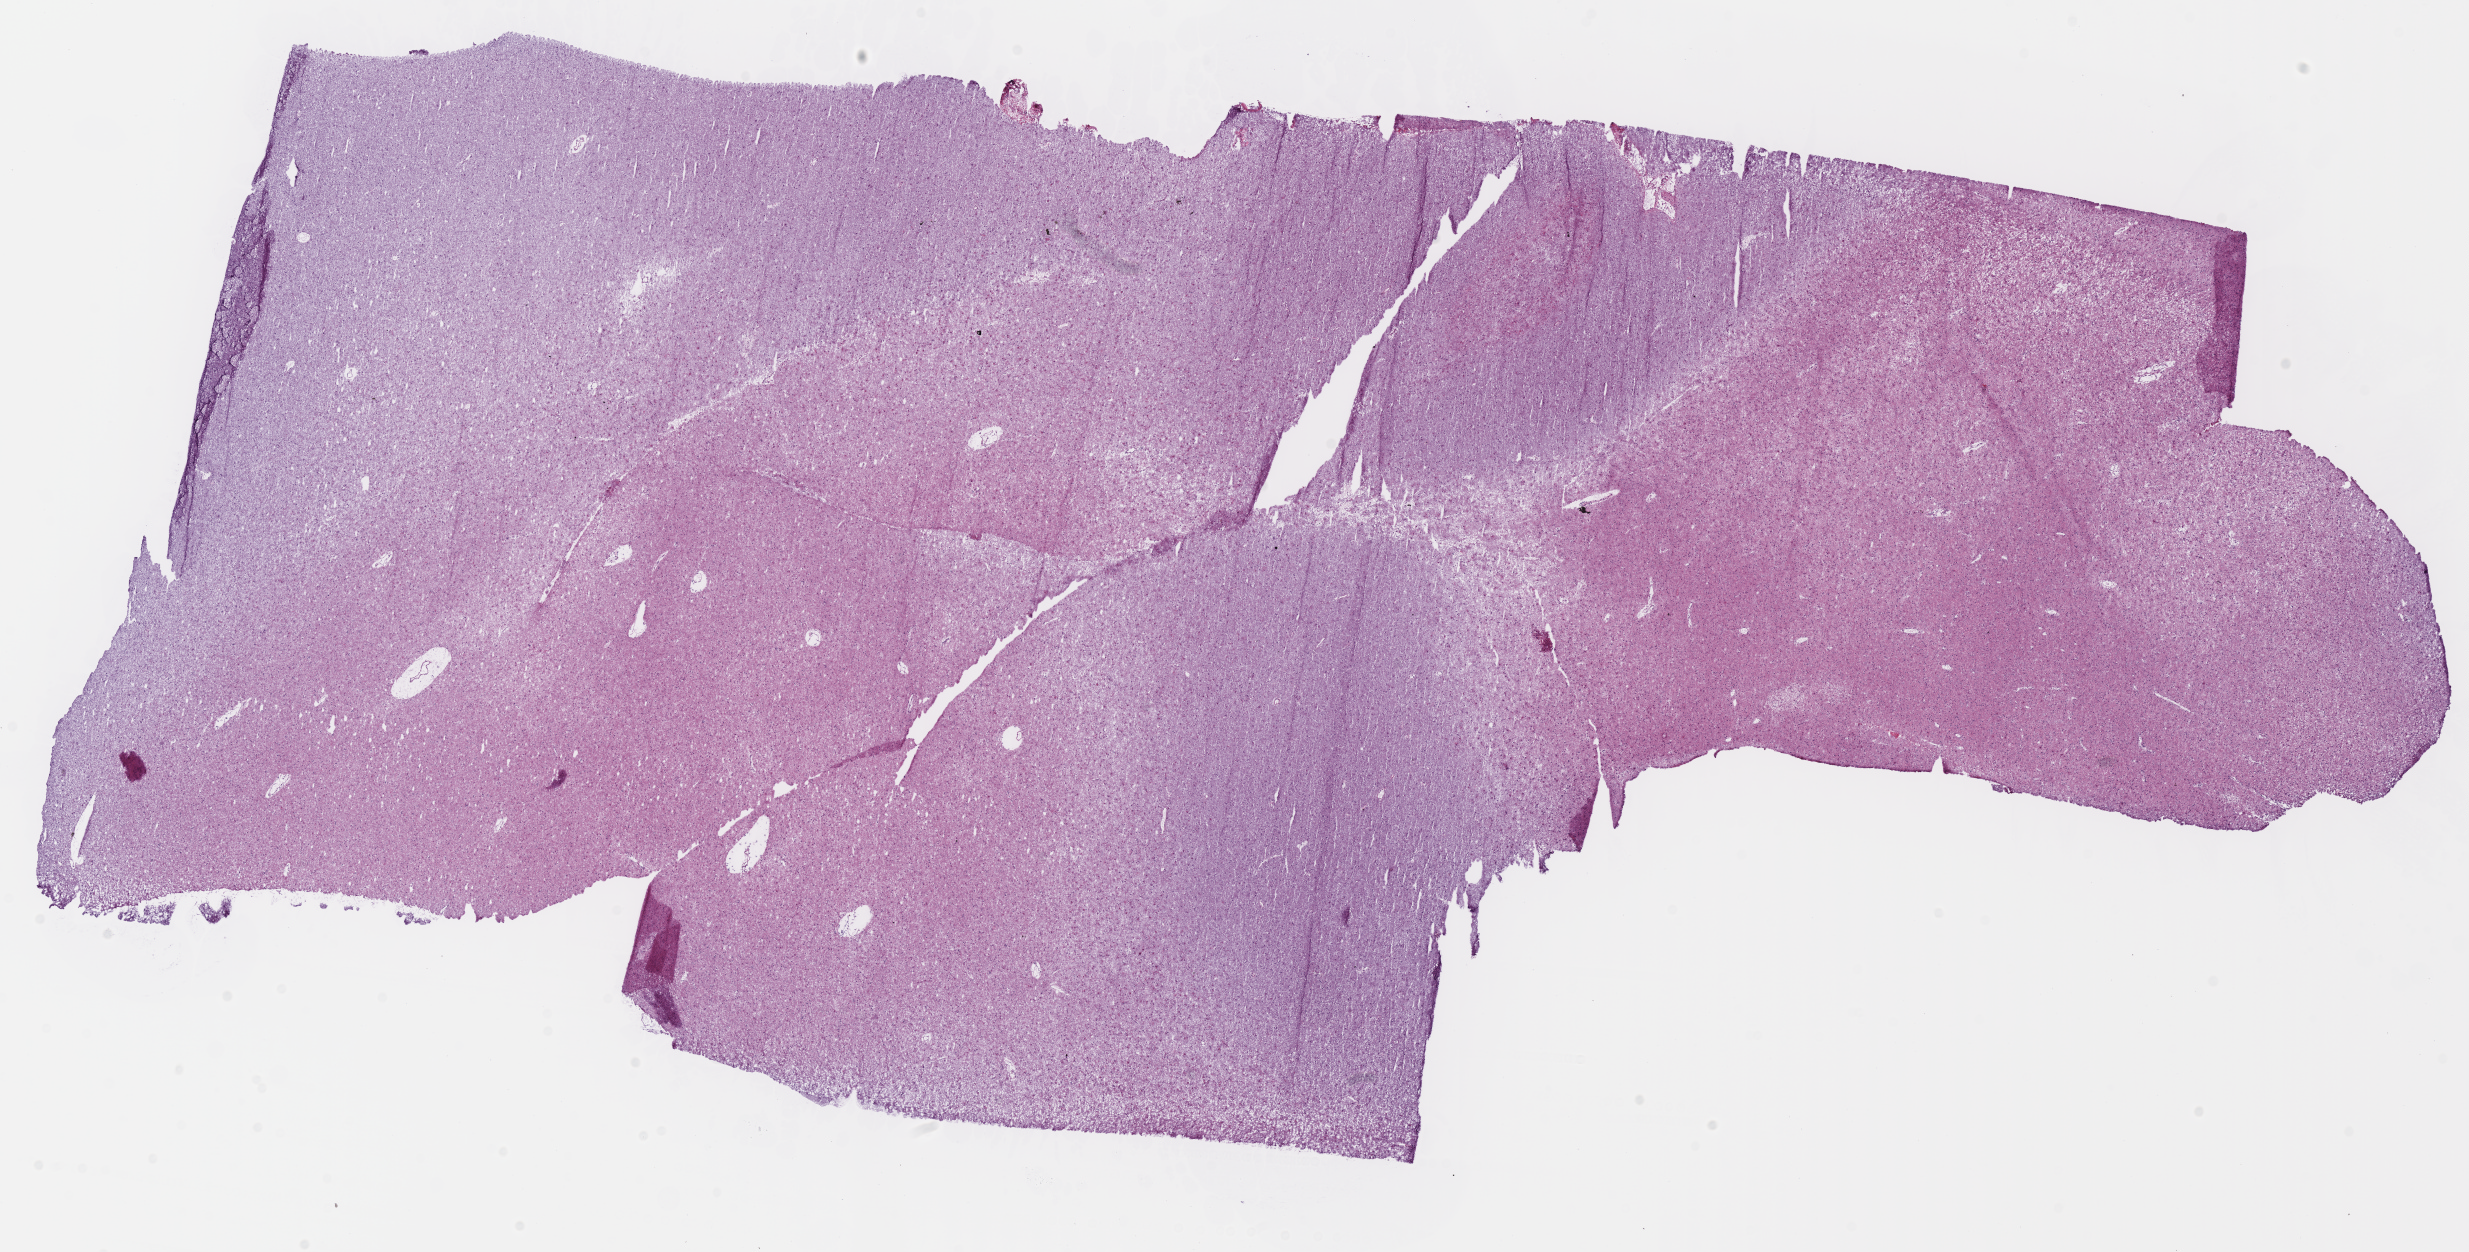
H&E-stained whole-slide image — a low-resolution overview of the entire scanned area, about 19.5 x 9.9 mm. Frozen section. Brain, primary tumour sample. Patient: female, age at initial diagnosis 61 years.
Pathologic diagnosis: Astrocytoma, NOS.